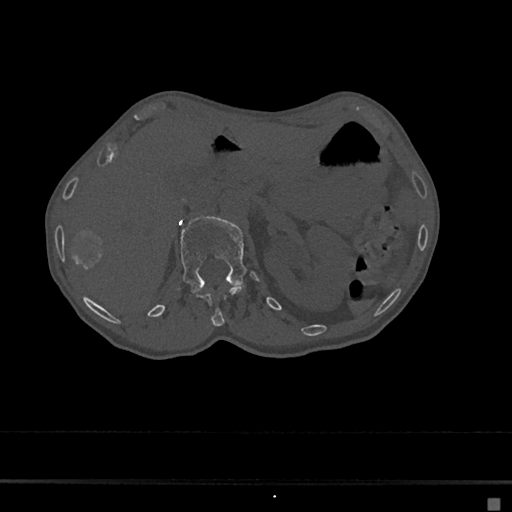
CT including the spine, one axial slice; slice 82 of 797 in the series (ordered by position); reconstruction kernel Br40s/3; bone window (W 1800 / L 400 HU); 0.5 mm slice thickness; 512 × 512 image matrix, field of view 360 × 360 mm. Patient: female, 68 years. From the clinical record (not read from this slice): primary cancer: renal.
Outlined on this slice (semi-automatic segmentation, software-assisted and operator-edited):
- L1 vertebra: box from (x=181, y=217) to (x=258, y=293) px
- T12 vertebra: (x=195, y=287)–(x=242, y=327)